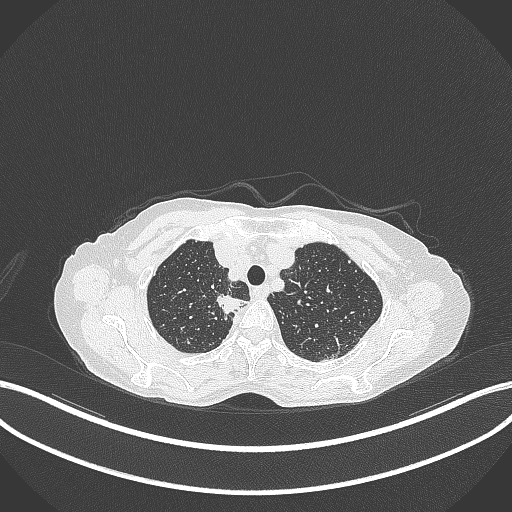
Chest CT, one axial slice. Position 312 of 403 along the scan axis. Reconstruction kernel B70f. 120 kVp. Lung window (W 1500 / L -600 HU). 1 mm slice thickness. 512 × 512 image matrix. Female patient, age 75 years. From the clinical record (not read from this slice): clinical TNM (as recorded): T1c N1 M1.
Structures marked on this image (bounding box drawn by a radiologist):
- lung tumour (recorded histology: adenocarcinoma): bounding box <212,288,250,318> (left, top, right, bottom; pixels)